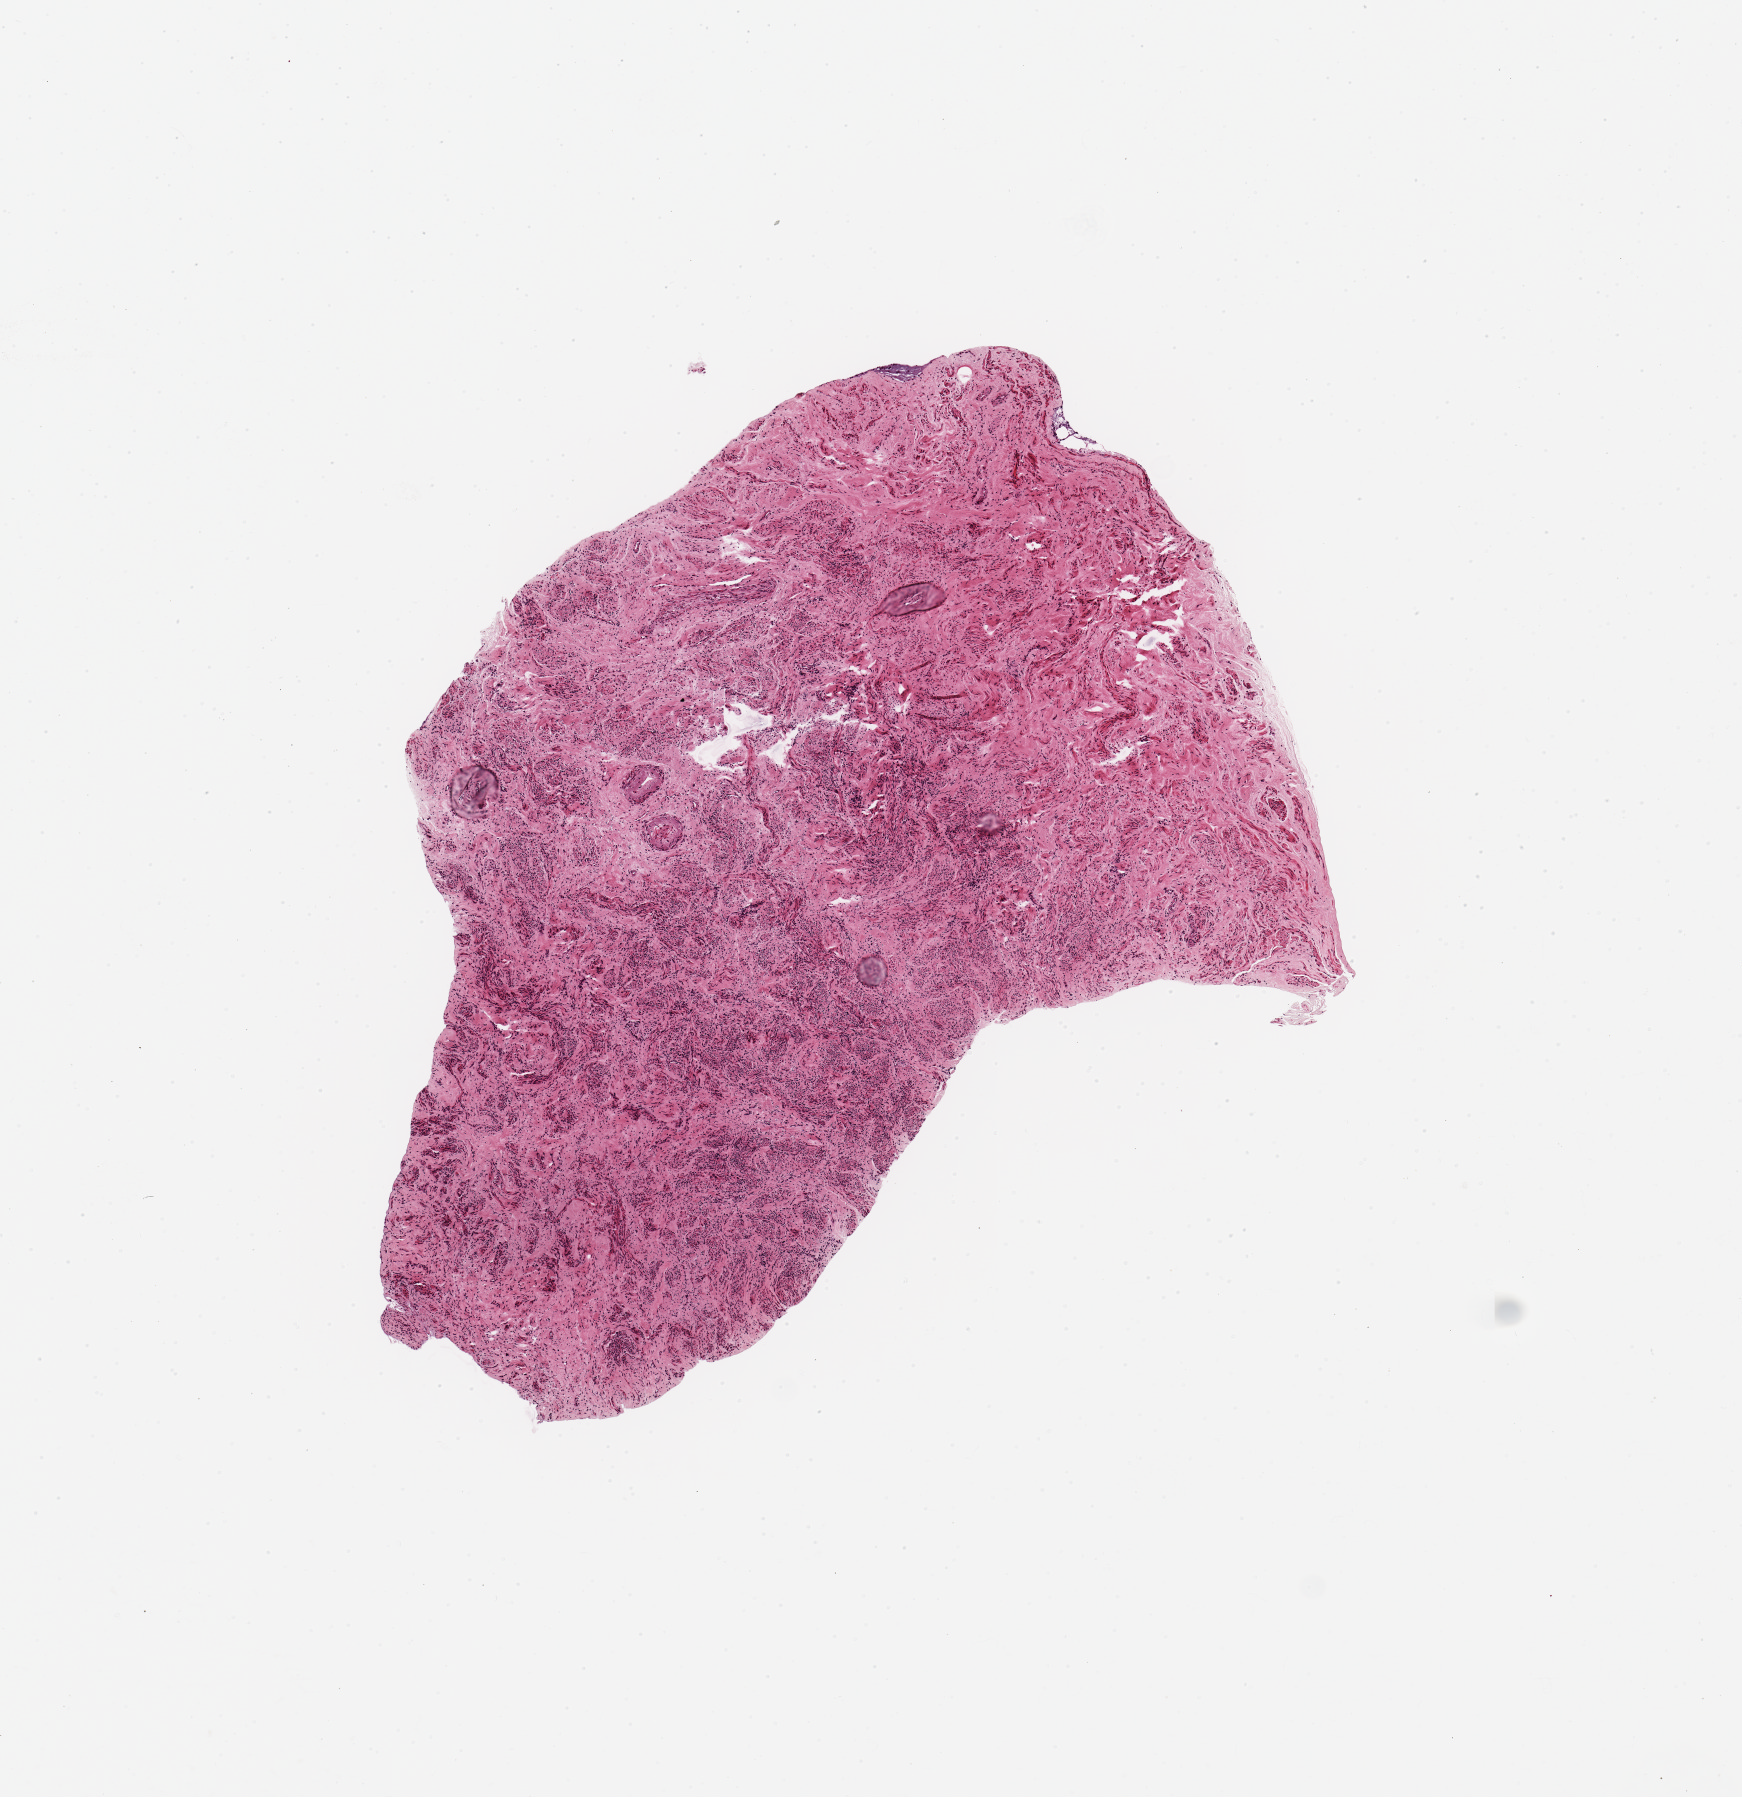
Whole-slide image, hematoxylin and eosin (H&E) stain — whole scanned area (about 6.9 x 7.1 mm, acquisition: 20x scan) shown as a low-resolution overview; PAXgene-fixed paraffin-embedded (PFPE) section; sampled site (target tissue): endocervix; donor tissue sample. Female donor.
Review note (as recorded): 4.5 x 2.5mm stromal aliquot. No glands present.